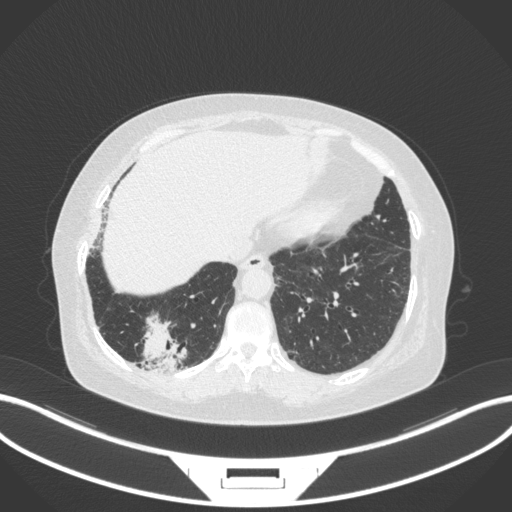
Chest CT, one axial slice; position 37 of 303 along the scan axis; 120 kVp; lung window (W 1500 / L -600 HU); 1 mm slice thickness; 512 × 512 image matrix, field of view 400 × 400 mm. Patient: female, 65 years. Case-level facts recorded for this patient, not image findings: clinical TNM (as recorded): T2b N1 M0; histopathological grade: G1.
Annotated regions visible in this slice (bounding box drawn by a radiologist):
- lung tumour (recorded histology: adenocarcinoma): bounding box [x1, y1, x2, y2] px = [133, 311, 189, 374]